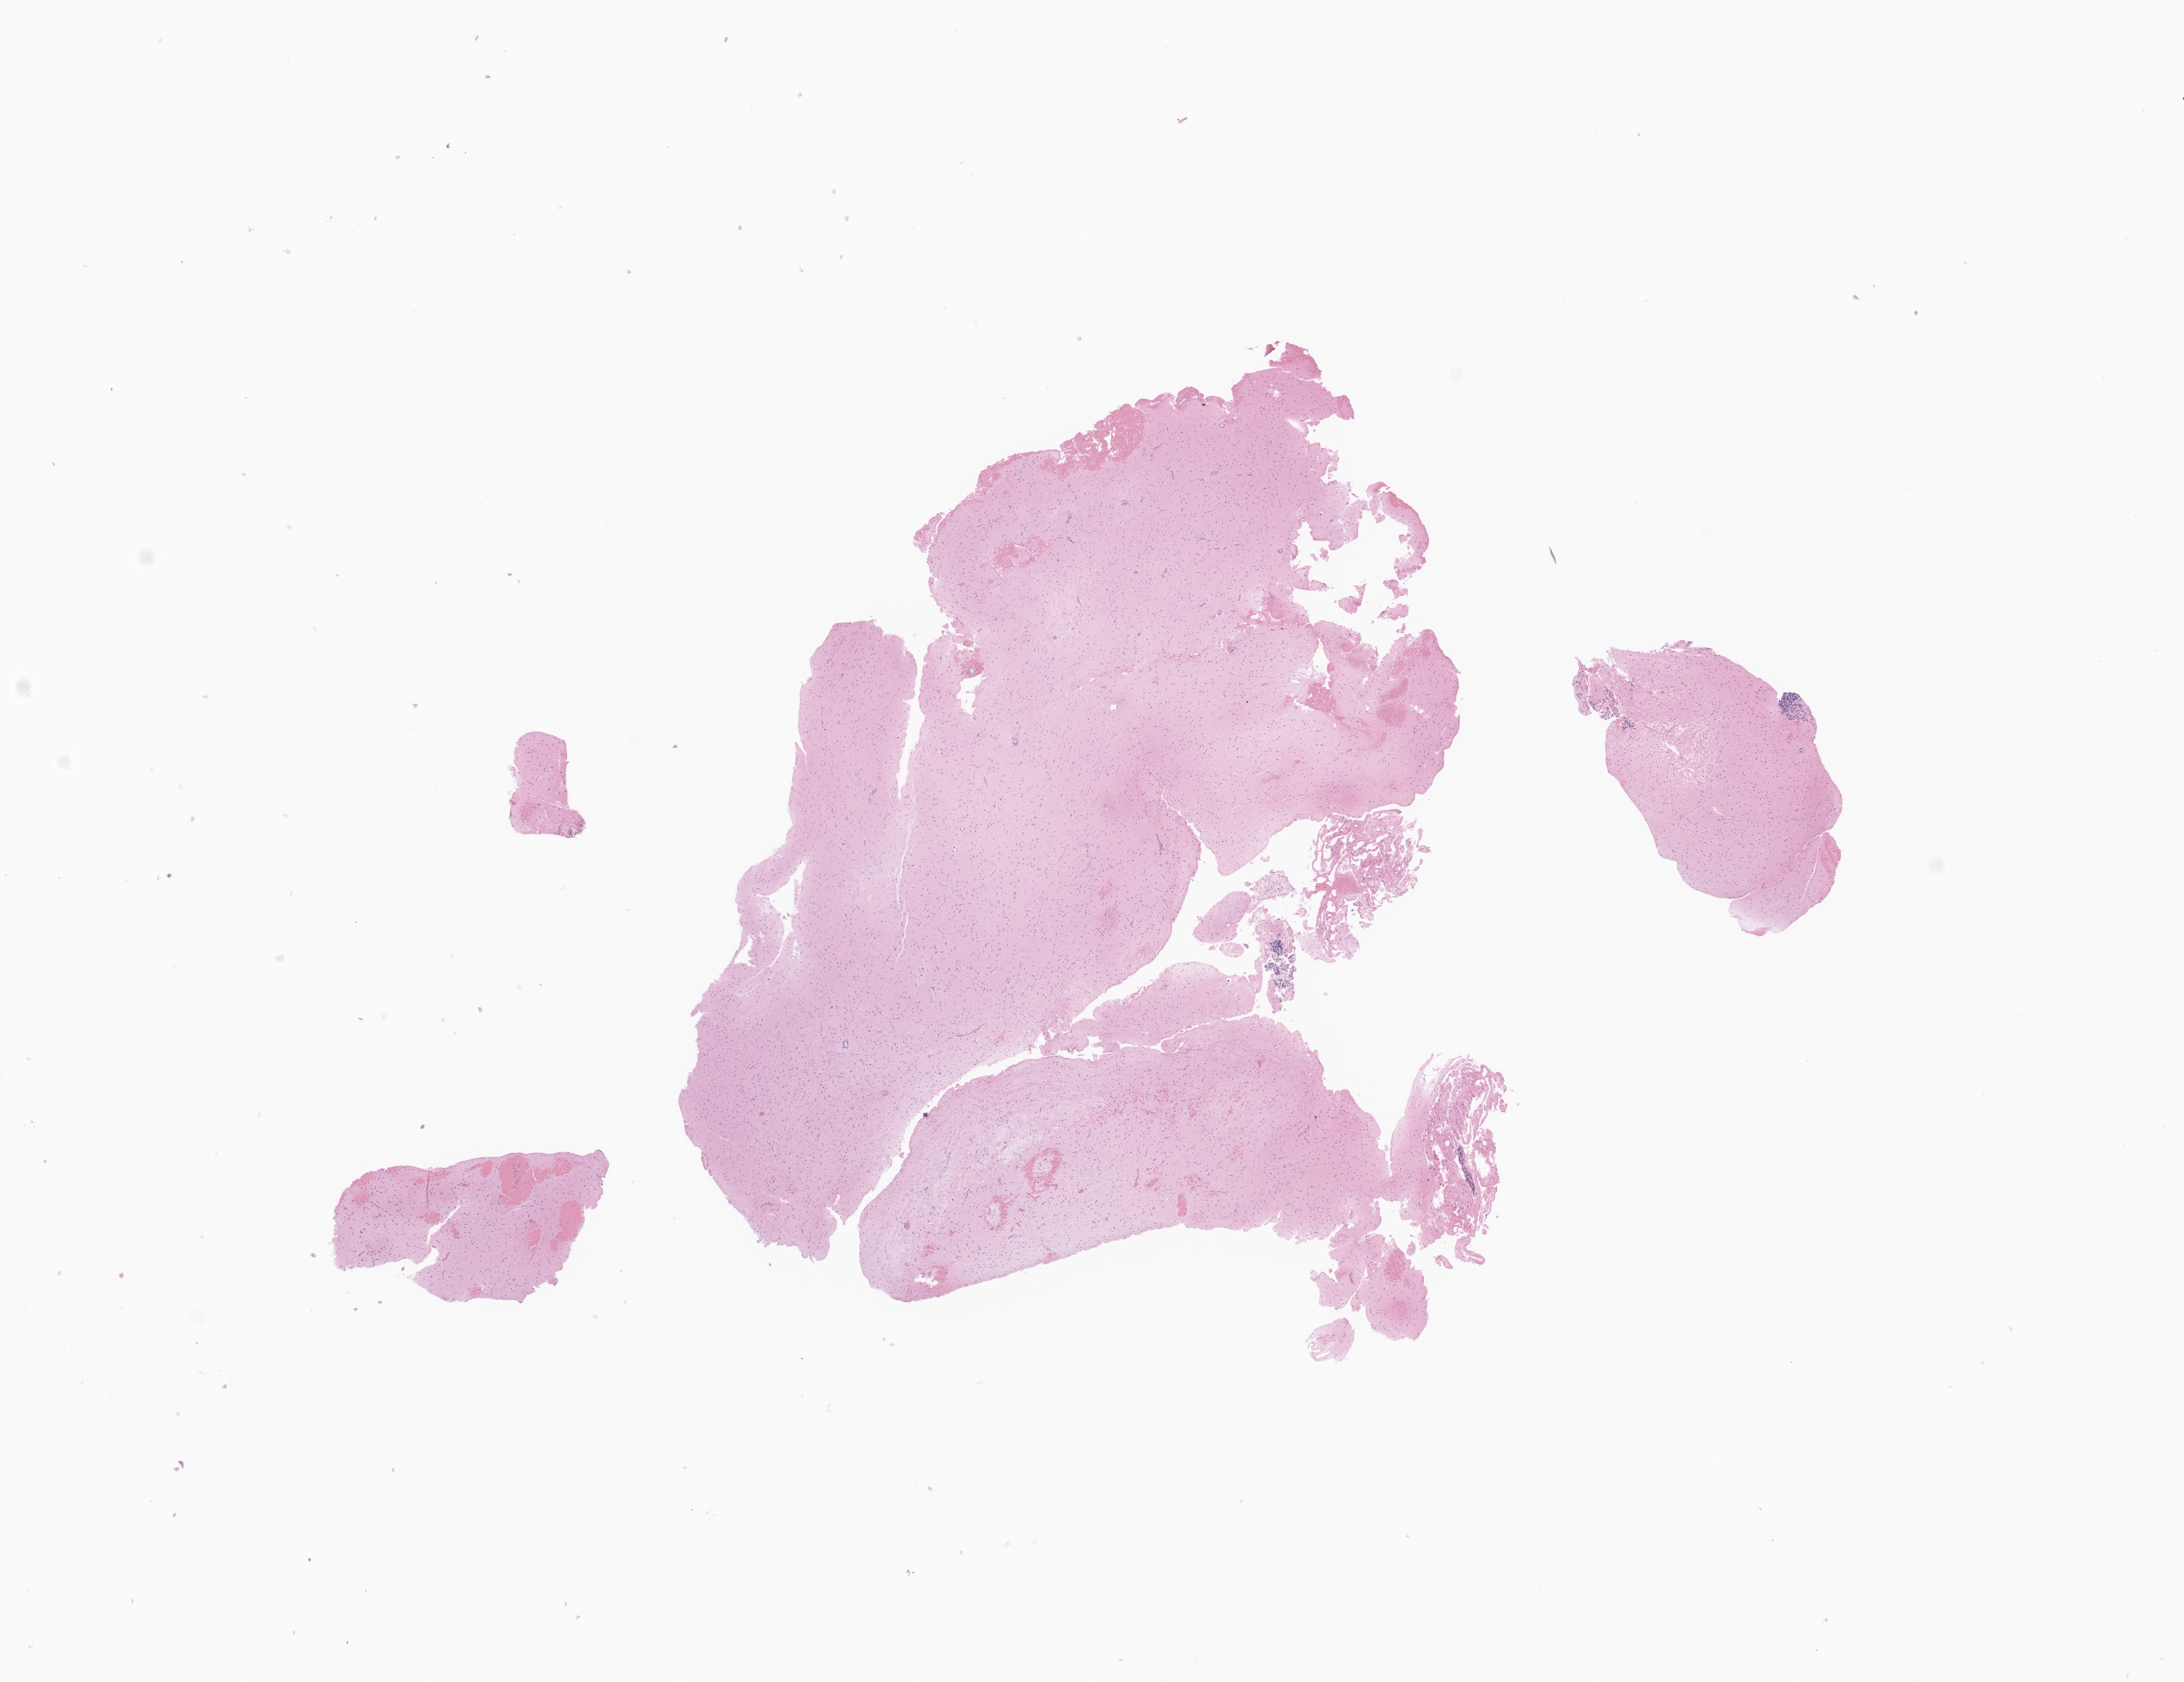
Haematoxylin and eosin whole-slide image of tumor tissue from the brain, low-resolution overview of the scanned area, about 12.8 x 9.9 mm; formalin-fixed paraffin-embedded section. Male patient, age 344 days.
* diagnosis: Neoplasm, uncertain whether benign or malignant